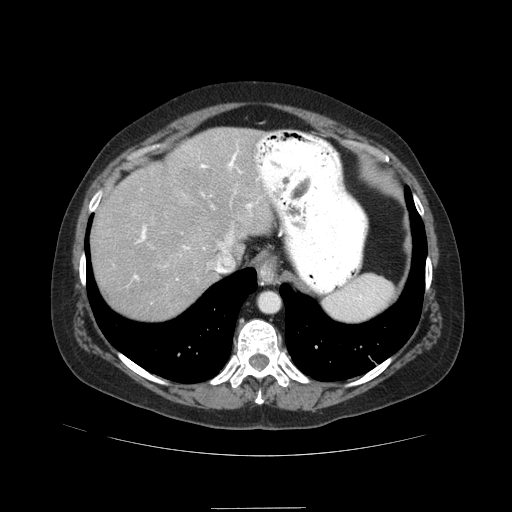
Contrast-enhanced abdominal CT (liver protocol), one axial slice. Slice 70 of 89 in the series (ordered by position). Reconstruction kernel STANDARD. Soft-tissue window (W 400 / L 40 HU). 512 × 512 image matrix, field of view 400 × 400 mm. From the clinical record (not read from this slice): diagnosis: hepatocellular carcinoma (patient treated with transarterial chemoembolisation; whether this scan precedes or follows treatment is not stated here); TNM stage (as recorded): Stage-IIIB; Child-Pugh class: A; tumour nodularity: multinodular.
Annotated regions visible in this slice (semi-automatic segmentation, software-assisted and operator-edited):
- abdominal aorta: bounding box [x1, y1, x2, y2] px = [260, 293, 278, 311]
- liver parenchyma outside the tumour (the mass and vessels are separate outlines, so this box may not span the whole liver): [90, 128, 267, 320]
- liver vessels: [134, 152, 253, 279]